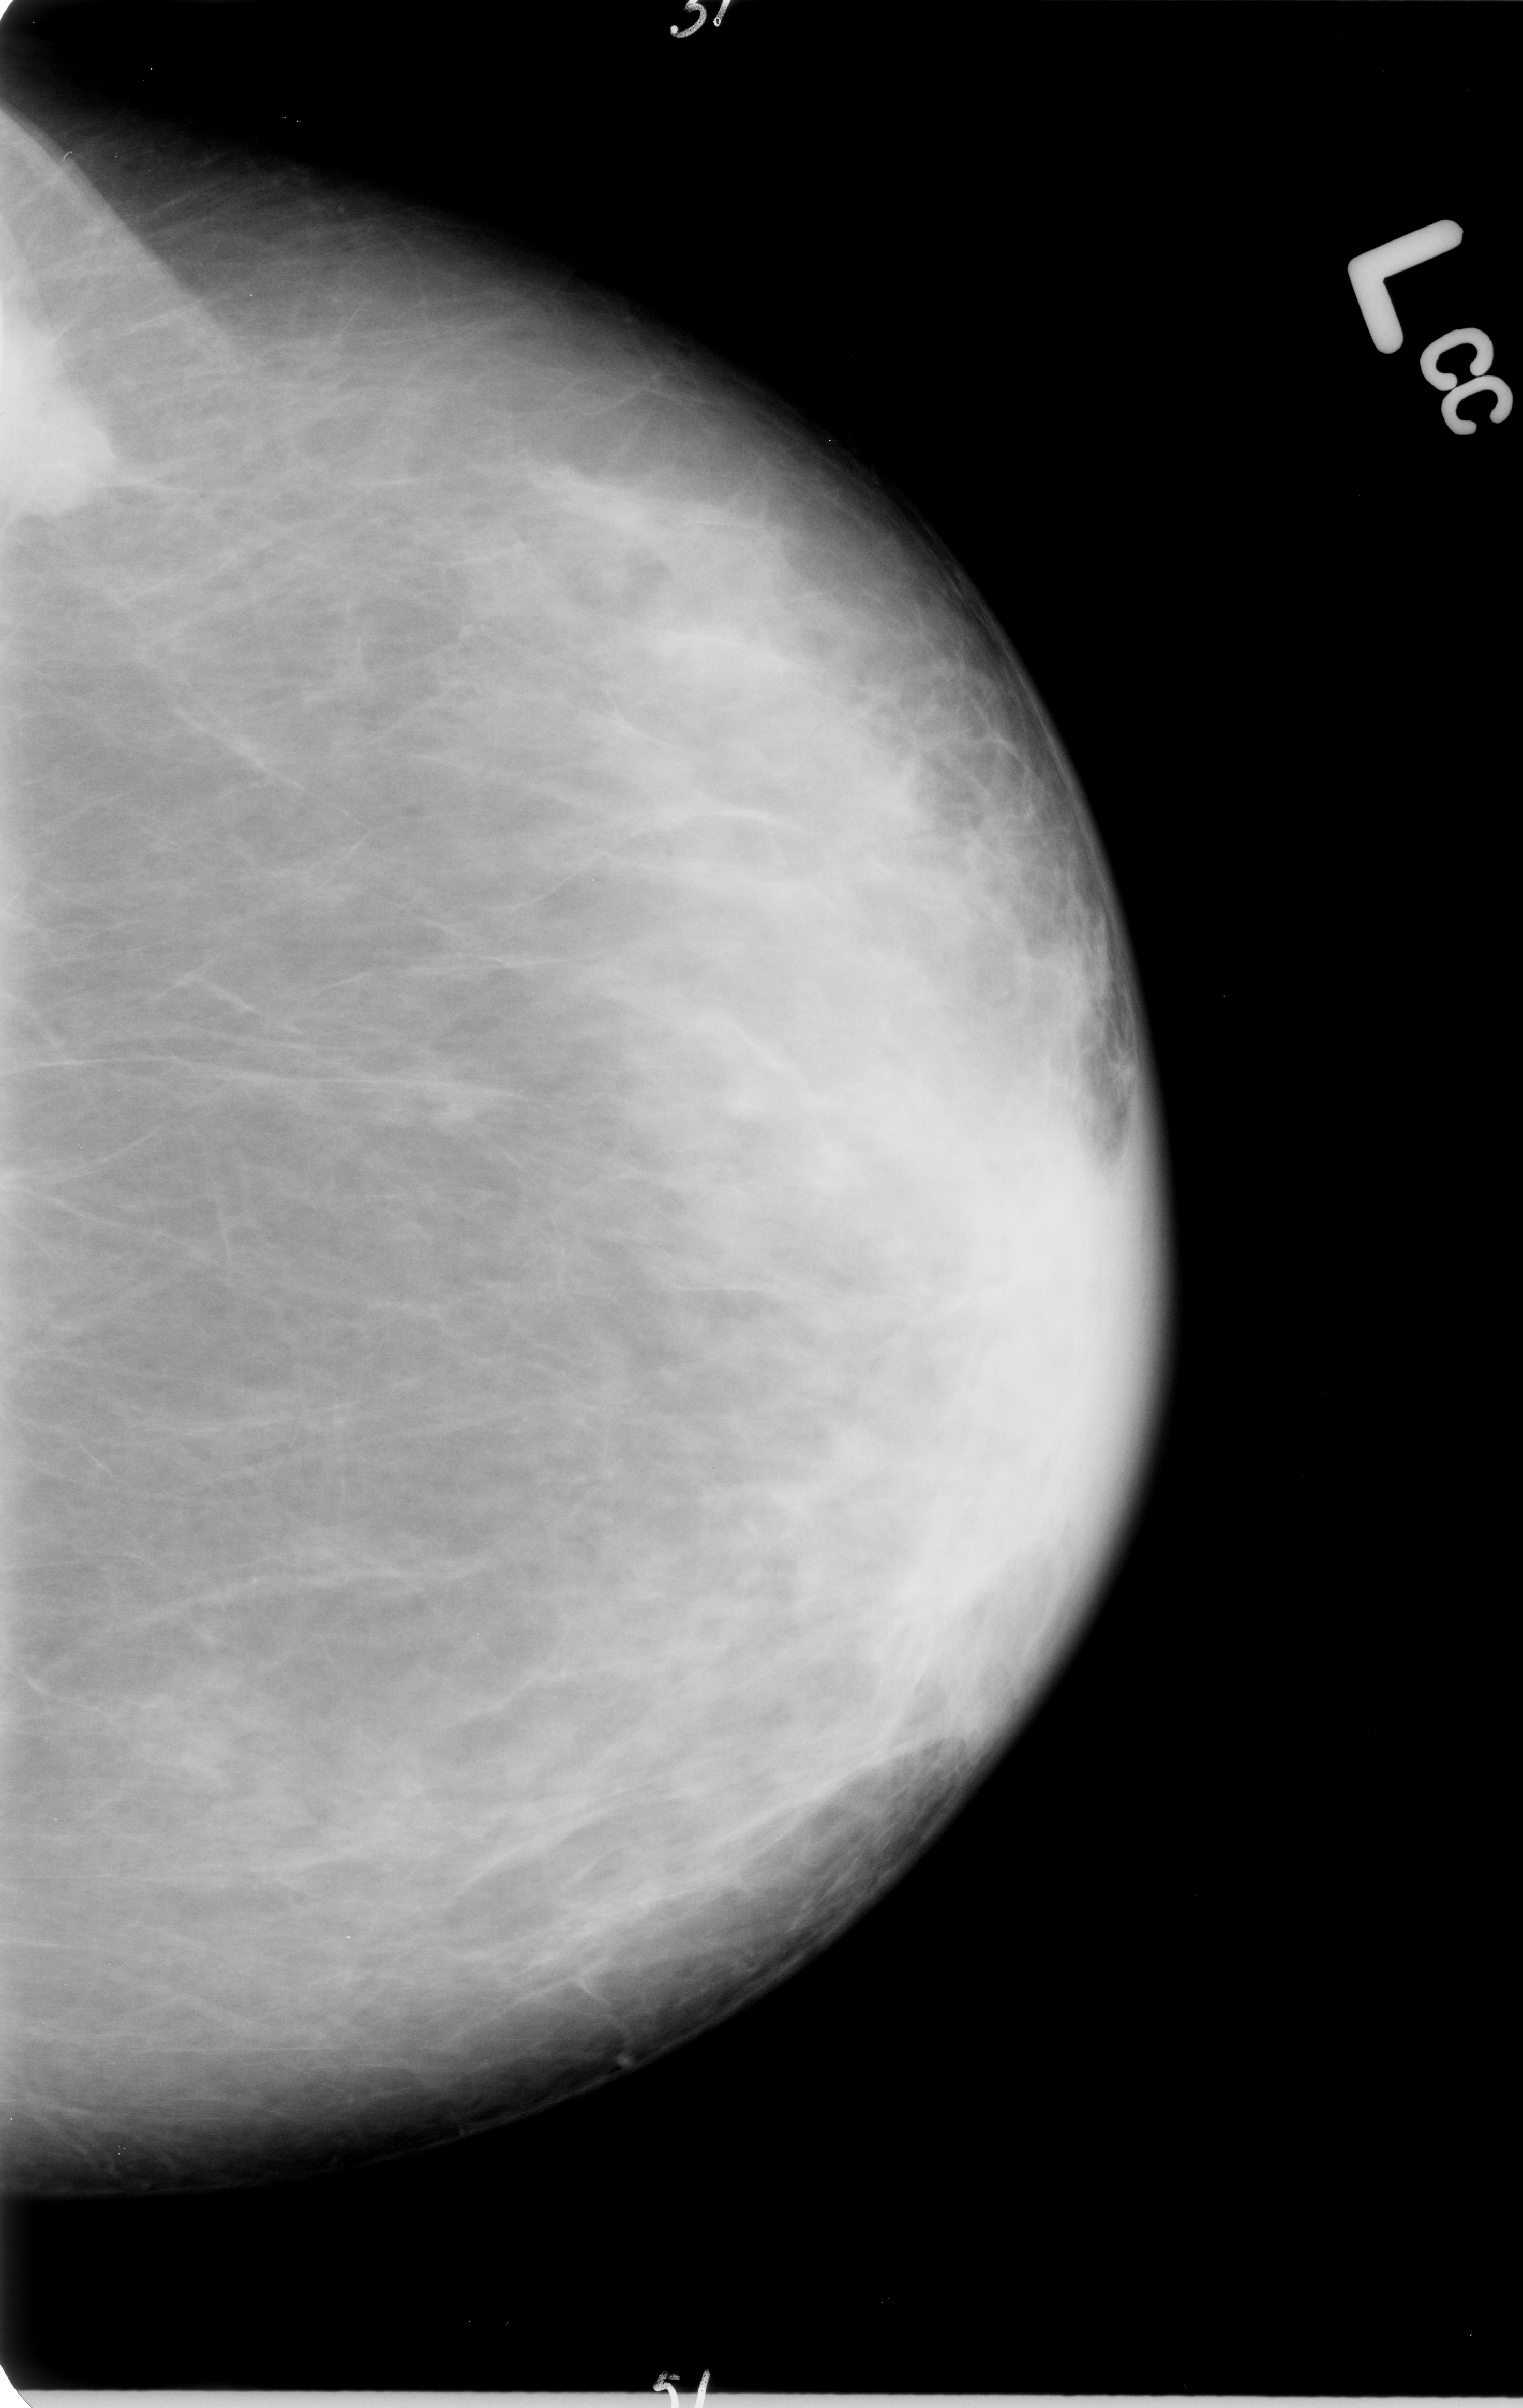
Scanned film-screen mammogram; left breast; craniocaudal (CC) view; BI-RADS breast density category 3 (scale 1–4).
Marked findings (only marked abnormalities are described; nothing is implied about the rest of the image): mass, shape irregular, margins spiculated; BI-RADS assessment category 4; subtlety rating 4 on a 1 (subtle) to 5 (obvious) scale; pathology (as recorded): malignant.